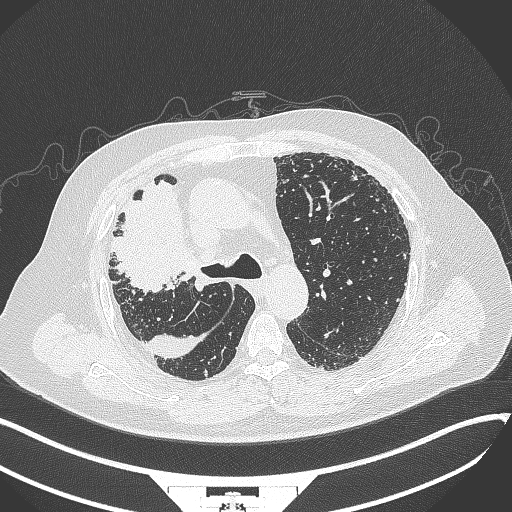
Chest CT, one axial slice. Slice 240 of 384 in the series (ordered by position). 120 kVp. Lung window (W 1500 / L -600 HU). 1 mm slice thickness. 512 × 512 image matrix, field of view 400 × 400 mm. Patient: male, 69 years. Case-level facts recorded for this patient, not image findings: clinical TNM (as recorded): T4 N3 M1.
Annotated regions visible in this slice (bounding box drawn by a radiologist):
- lung tumour (recorded histology: adenocarcinoma): bounding box <101,175,194,296> (left, top, right, bottom; pixels)